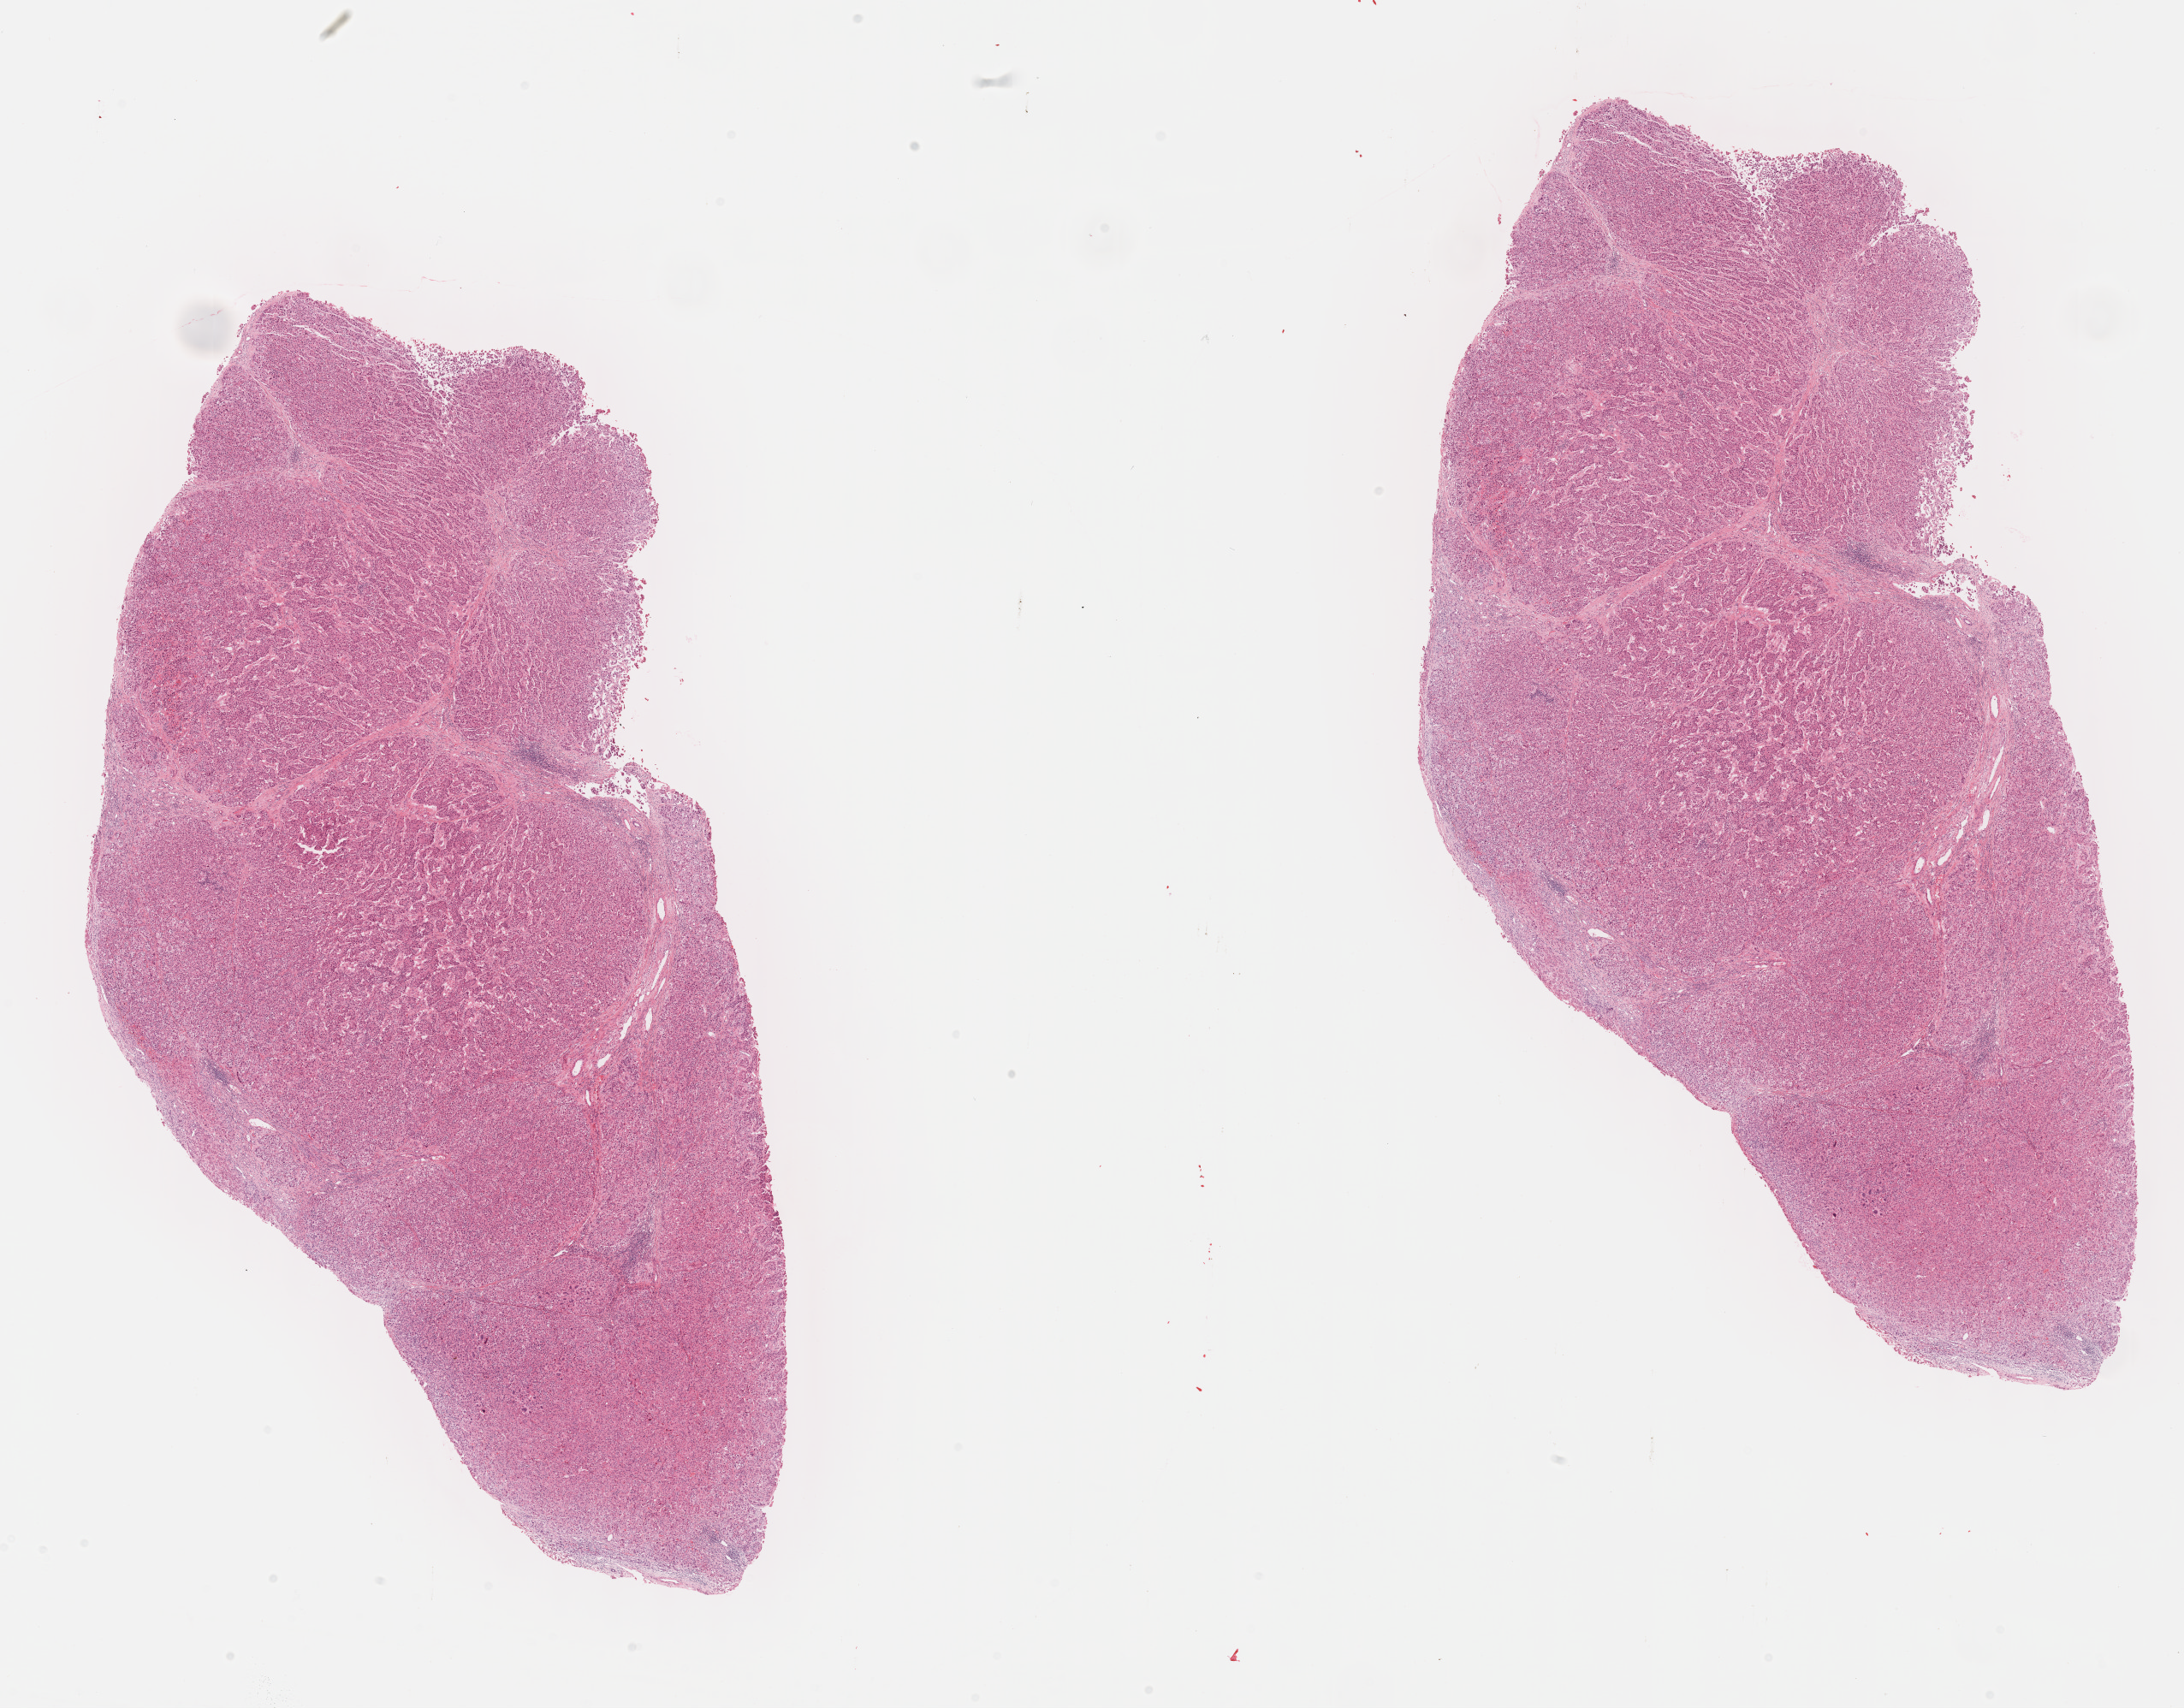
Whole-slide histology image, H&E-stained, whole scanned area (about 20.6 x 16.1 mm, from a 40x scan) shown as a low-resolution overview; formalin-fixed paraffin-embedded (FFPE) diagnostic section; primary tumour sample from the liver. Male patient; age at initial diagnosis 59 years. Histologic grade: G3 (poorly differentiated).
* pathologic diagnosis: Hepatocellular carcinoma, NOS
* AJCC pathologic stage: I (7th edition)